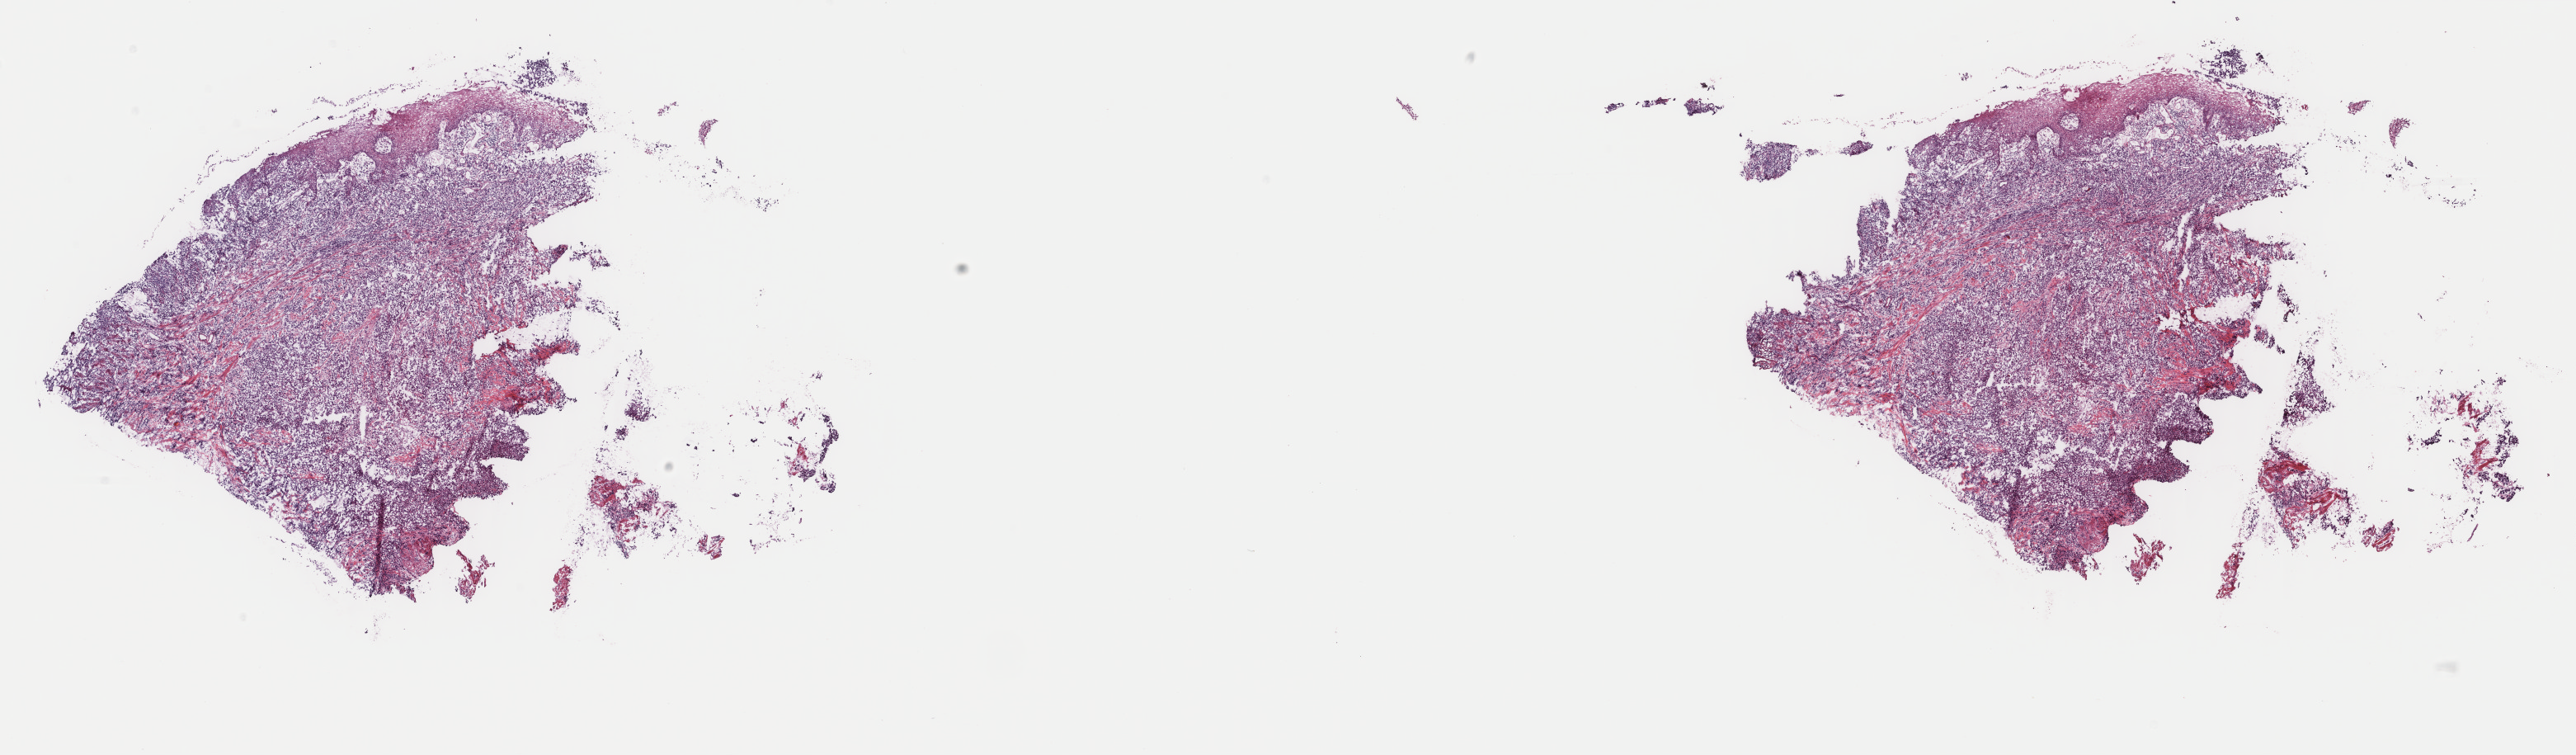
H&E whole-slide image — low-resolution overview of the scanned area, about 24.8 x 7.3 mm (slide scanned at 40x); frozen section; sample: primary tumour, esophagus. Male, age 50 years at initial diagnosis. Histologic grade: G2 (moderately differentiated). Composition of this section per pathologist review: tumour cells 72%, tumour nuclei 84%, normal cells 4%, stromal cells 21%, necrosis 3%. Infiltration values recorded for this section: lymphocyte infiltration 15%, monocyte infiltration 0%, neutrophil infiltration 0%.
Pathologic diagnosis: Squamous cell carcinoma, NOS. AJCC pathologic stage: III (6th edition).